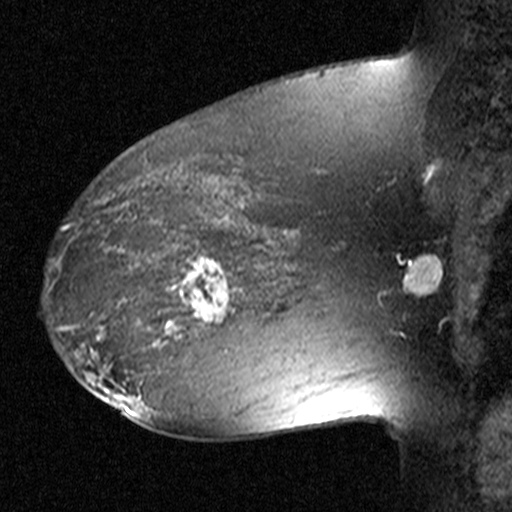
Breast MRI (dynamic contrast-enhanced), one sagittal slice. Slice 29 of 44 in the series (ordered by position). Dynamic contrast-enhanced study with each time point stored as its own series, time point 2 of 3 at this slice position (early post-contrast, ordered by acquisition time). 1.5 T. TE 4.5 ms, TR 11 ms. 3 mm slice thickness. 512 × 512 image matrix. Female patient, age 38 years. From the clinical record (not read from this slice): setting: breast cancer imaged before/during neoadjuvant chemotherapy; receptor status: HR-positive, HER2-negative.
Structures marked on this image (semi-automatic segmentation, software-assisted and operator-edited):
- analysis volume of interest (the breast-tissue region the enhancement analysis was run in; not a lesion): bounding box [x1, y1, x2, y2] px = [152, 236, 253, 335]
- tumour enhancement mask (voxels above the 90 % enhancement threshold inside the analysis volume of interest): [167, 253, 233, 333]